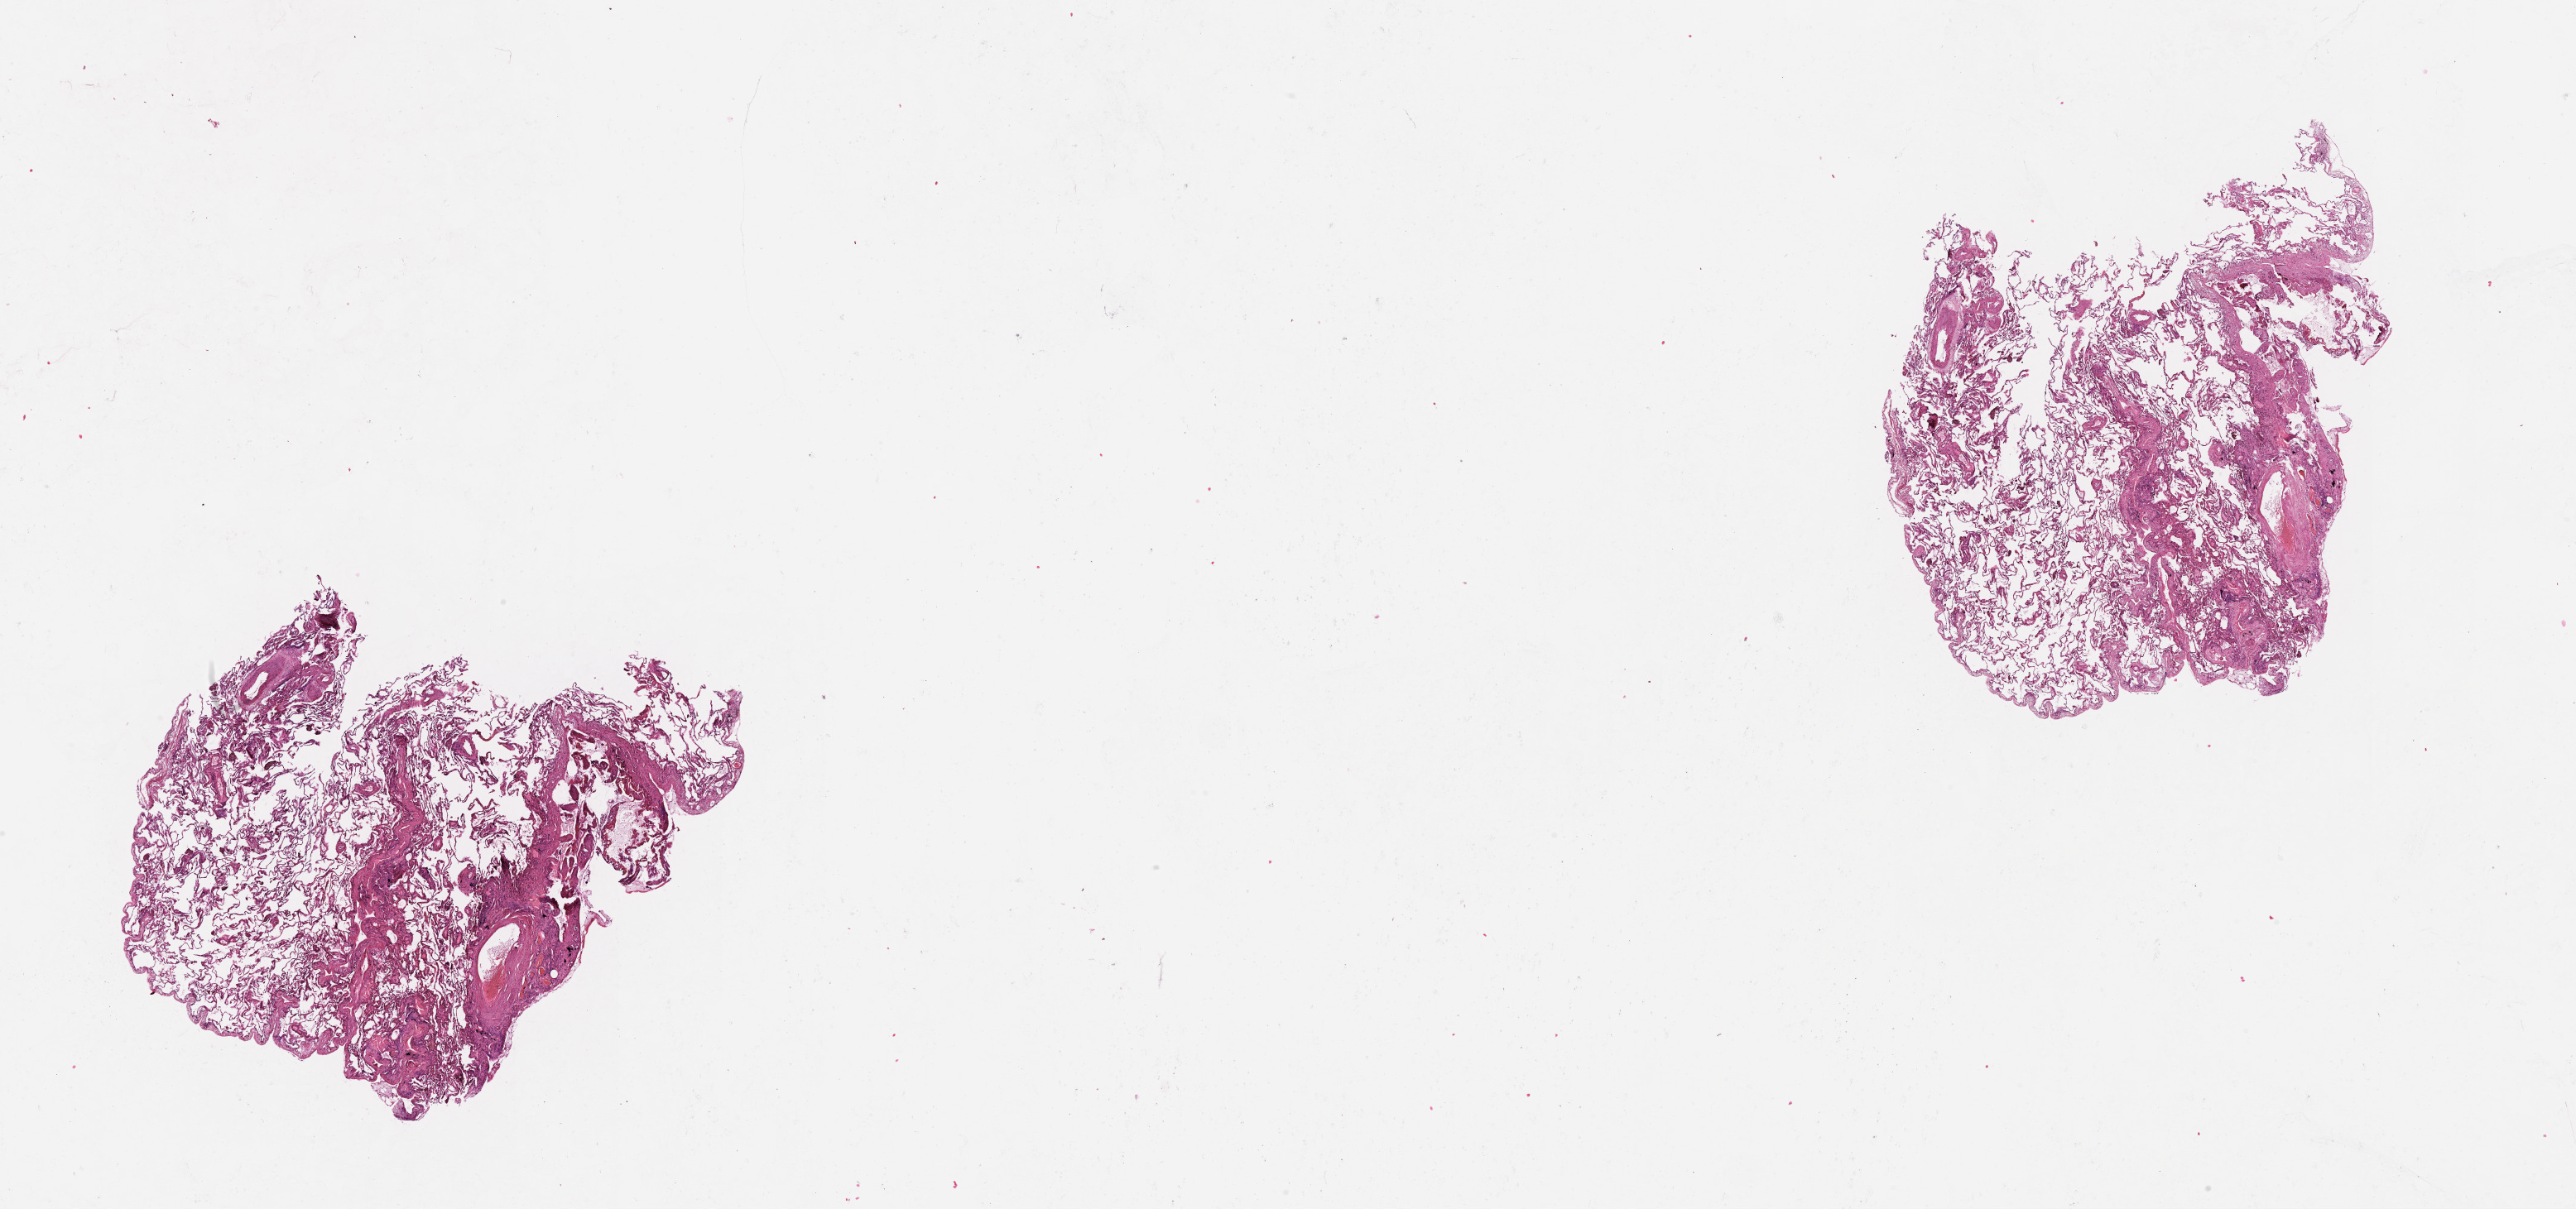
Whole-slide histology image, H&E — a low-resolution overview of the entire scanned area, about 25.1 x 11.8 mm (acquisition: 20x scan). Lung, normal (non-tumour) tissue. 80-year-old male patient.
* this section: normal (non-tumour) tissue from the same patient
* patient diagnosis (cohort enrolment): squamous cell carcinoma (lung)